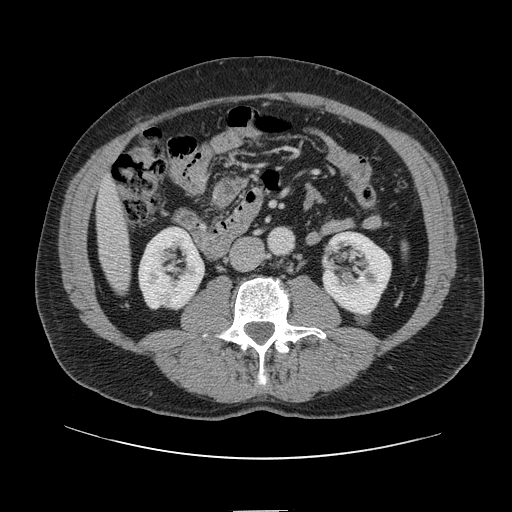
Contrast-enhanced abdominal CT, one axial slice. Slice 18 of 161 in the series (ordered by position). 120 kVp. Intravenous contrast given. Soft-tissue window (W 400 / L 40 HU). 2.5 mm slice thickness. 512 × 512 image matrix, field of view 412 × 412 mm. Male patient, age 66 years. From the clinical record (not read from this slice): diagnosis: colorectal cancer liver metastases, imaged before liver resection; multiple liver metastases: no.
Outlined on this slice (expert manual segmentation):
- liver: box from (x=97, y=181) to (x=130, y=292) px
- planned liver remnant (the part of the liver to remain after resection): (x=97, y=181)–(x=125, y=249)